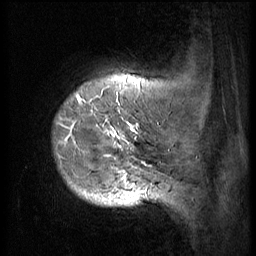
Breast MRI (dynamic contrast-enhanced), one sagittal slice. Slice 10 of 56 in the series (ordered by position). 3 images stored at this slice position (order not interpretable as contrast timing). 1.5 T. TE 4.2 ms, TR 9 ms. 2.5 mm slice thickness. 256 × 256 image matrix, field of view 180 × 180 mm. Patient: female, 49 years. Case-level facts recorded for this patient, not image findings: setting: breast cancer imaged before/during neoadjuvant chemotherapy; receptor status: HER2-positive.
Annotated regions visible in this slice (semi-automatically segmented with operator editing):
- analysis volume of interest (the breast-tissue region the enhancement analysis was run in; not a lesion): bounding box (x1, y1, x2, y2) in pixels: (49, 79, 152, 203)
- tumour enhancement mask (voxels above the 140 % enhancement threshold inside the analysis volume of interest): (67, 94, 150, 201)